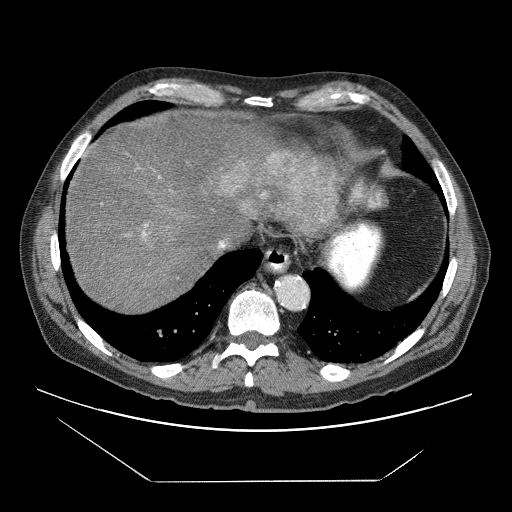
Contrast-enhanced abdominal CT (liver protocol), one axial slice; slice 62 of 83 in the series (ordered by position); reconstruction kernel STANDARD; soft-tissue window (W 400 / L 40 HU); 512 × 512 image matrix, field of view 420 × 420 mm. Case-level facts recorded for this patient, not image findings: diagnosis: hepatocellular carcinoma (patient treated with transarterial chemoembolisation; whether this scan precedes or follows treatment is not stated here); TNM stage (as recorded): Stage-IVB; Child-Pugh class: B; tumour differentiation: poorly differentiated.
Annotated regions visible in this slice (semi-automatically segmented with operator editing):
- liver parenchyma outside the tumour (the mass and vessels are separate outlines, so this box may not span the whole liver): box from (x=66, y=114) to (x=338, y=312) px
- mass: (x=219, y=156)–(x=338, y=231)
- liver vessels: (x=84, y=153)–(x=334, y=239)